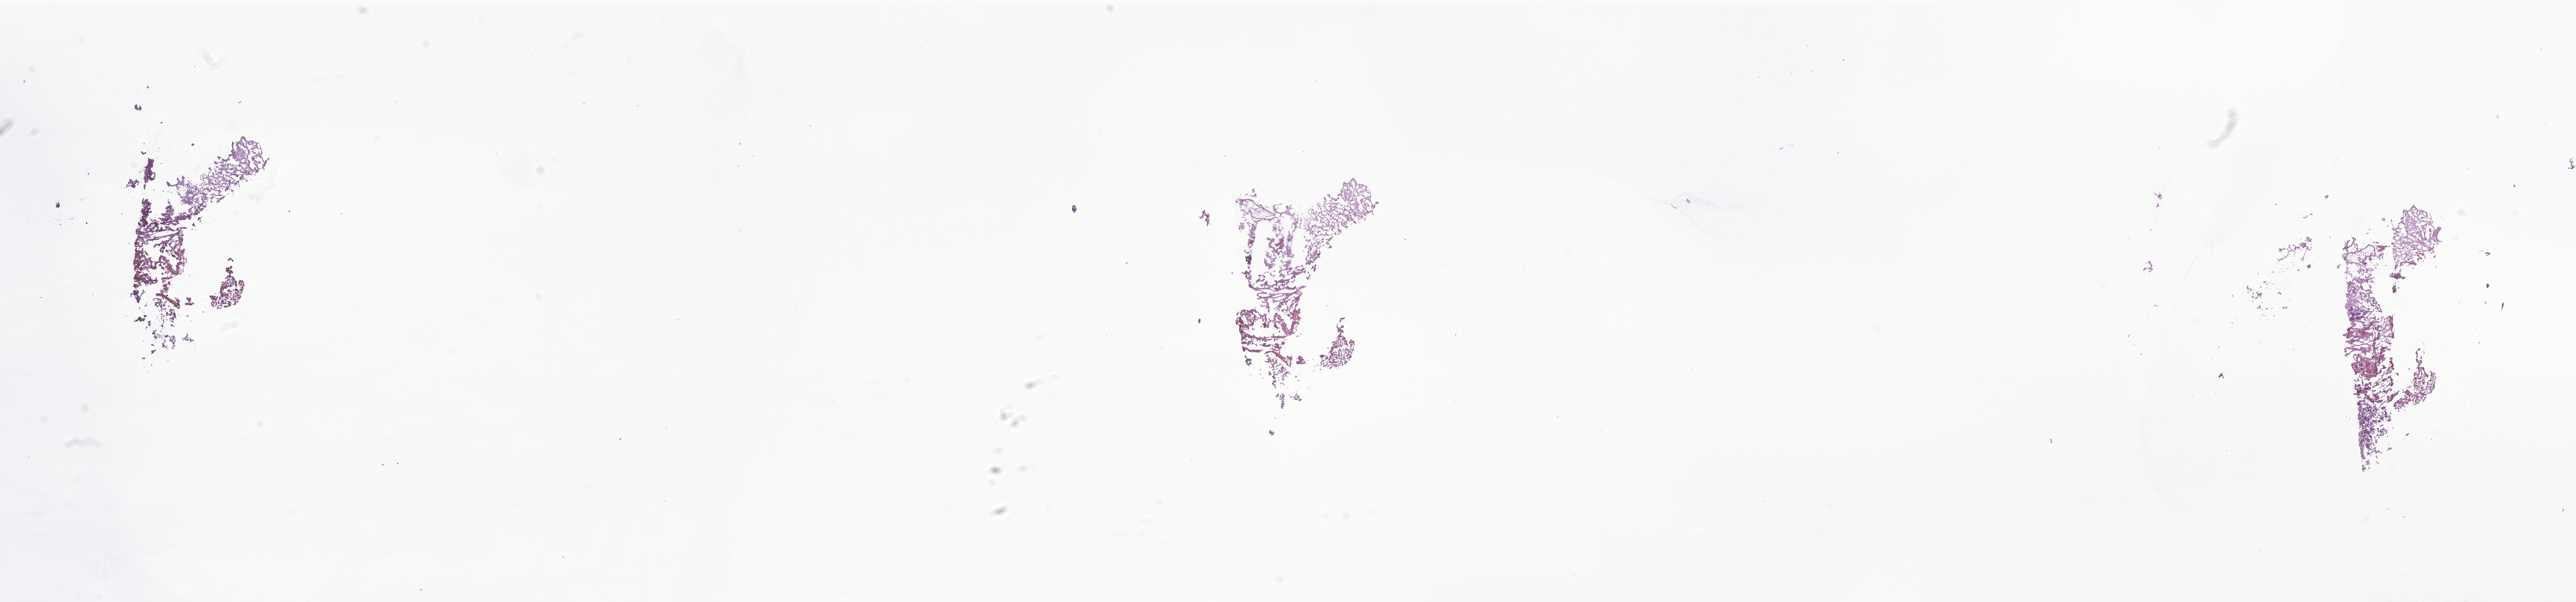
Digitized hematoxylin and eosin (H&E)-stained section of tumor tissue from the brain — shown as a low-resolution overview of the whole scanned area (about 35.5 x 8.3 mm); cryosection (OCT / tissue freezing medium). Patient female; age 145 months (12 years 1 month).
• diagnosis (ICD-O-3 morphology term): Embryonal carcinoma, NOS